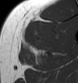
MRI of an extremity soft-tissue mass, one axial slice. Position 35 of 43 along the scan axis. MR volume resampled by the dataset authors to the PET/CT grid (not the native acquisition matrix). 78 × 83 image matrix. Male patient. From the clinical record (not read from this slice): histological type: pleiomorphic leiomyosarcoma; grade: high; site of the primary tumour: left thigh.
Structures marked on this image (expert contour drawn on MRI and transferred to this co-registered scan by the dataset authors):
- gross tumour volume including surrounding oedema: bounding box (x1, y1, x2, y2) in pixels: (22, 30, 39, 52)